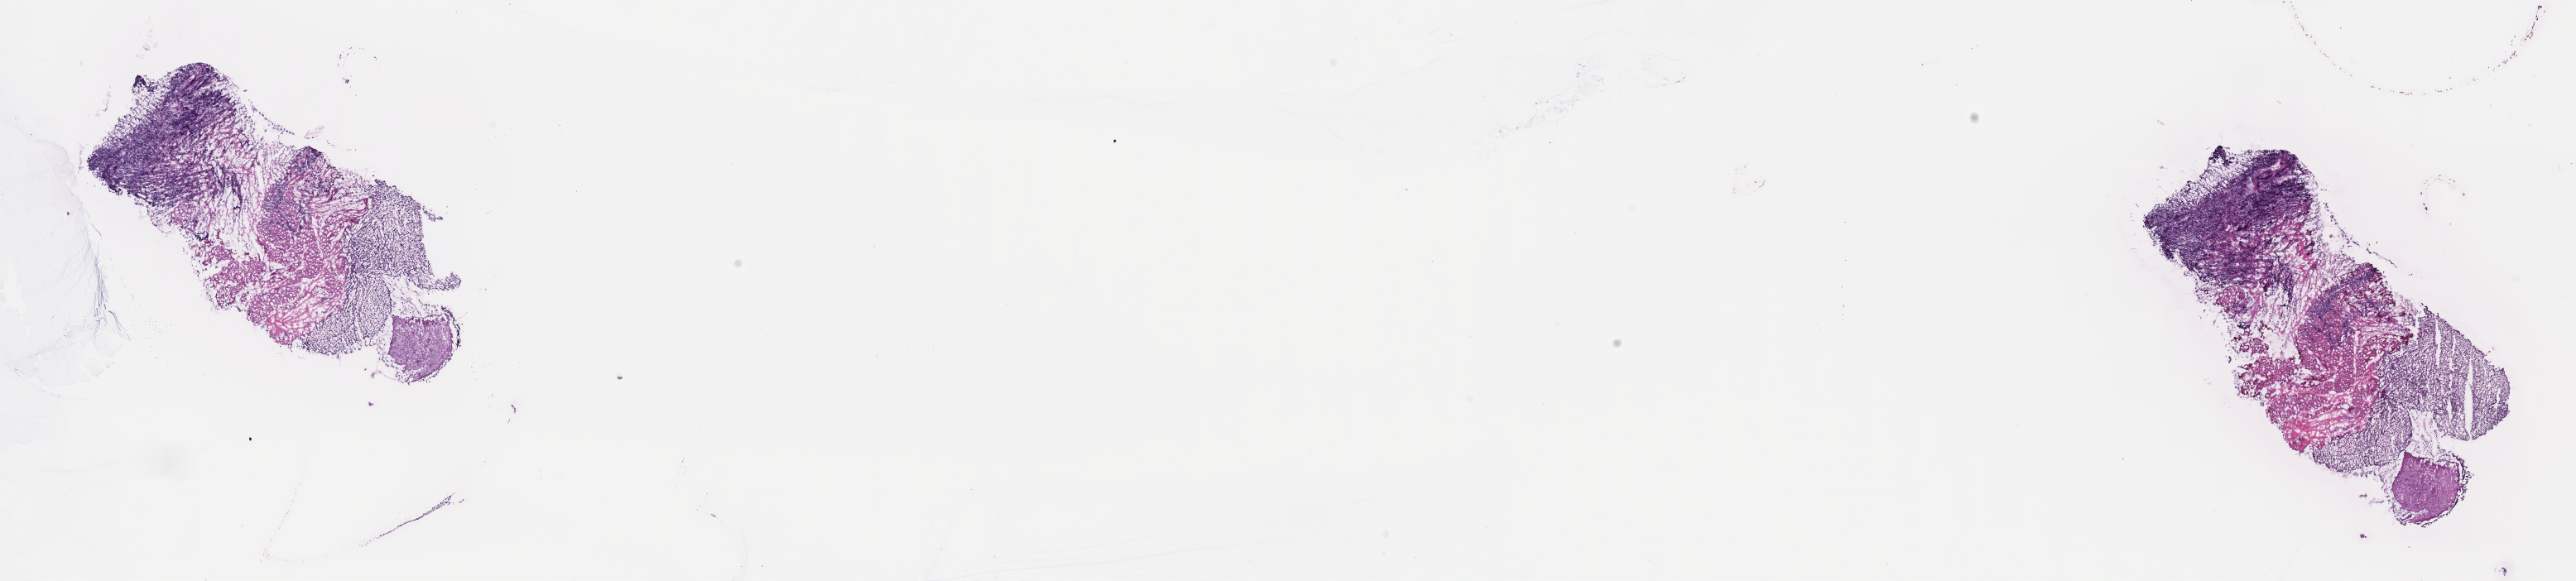
Whole-slide image, haematoxylin and eosin stain — shown as a low-resolution overview of the whole scanned area (about 25.2 x 5.7 mm), cryosection, primary tumor, anatomic site: cranium. Female, age 6 years at initial diagnosis. Slide review estimates, as recorded: tumor cells 40%, tumor nuclei 60%.
Histologic diagnosis: Burkitt lymphoma, NOS.